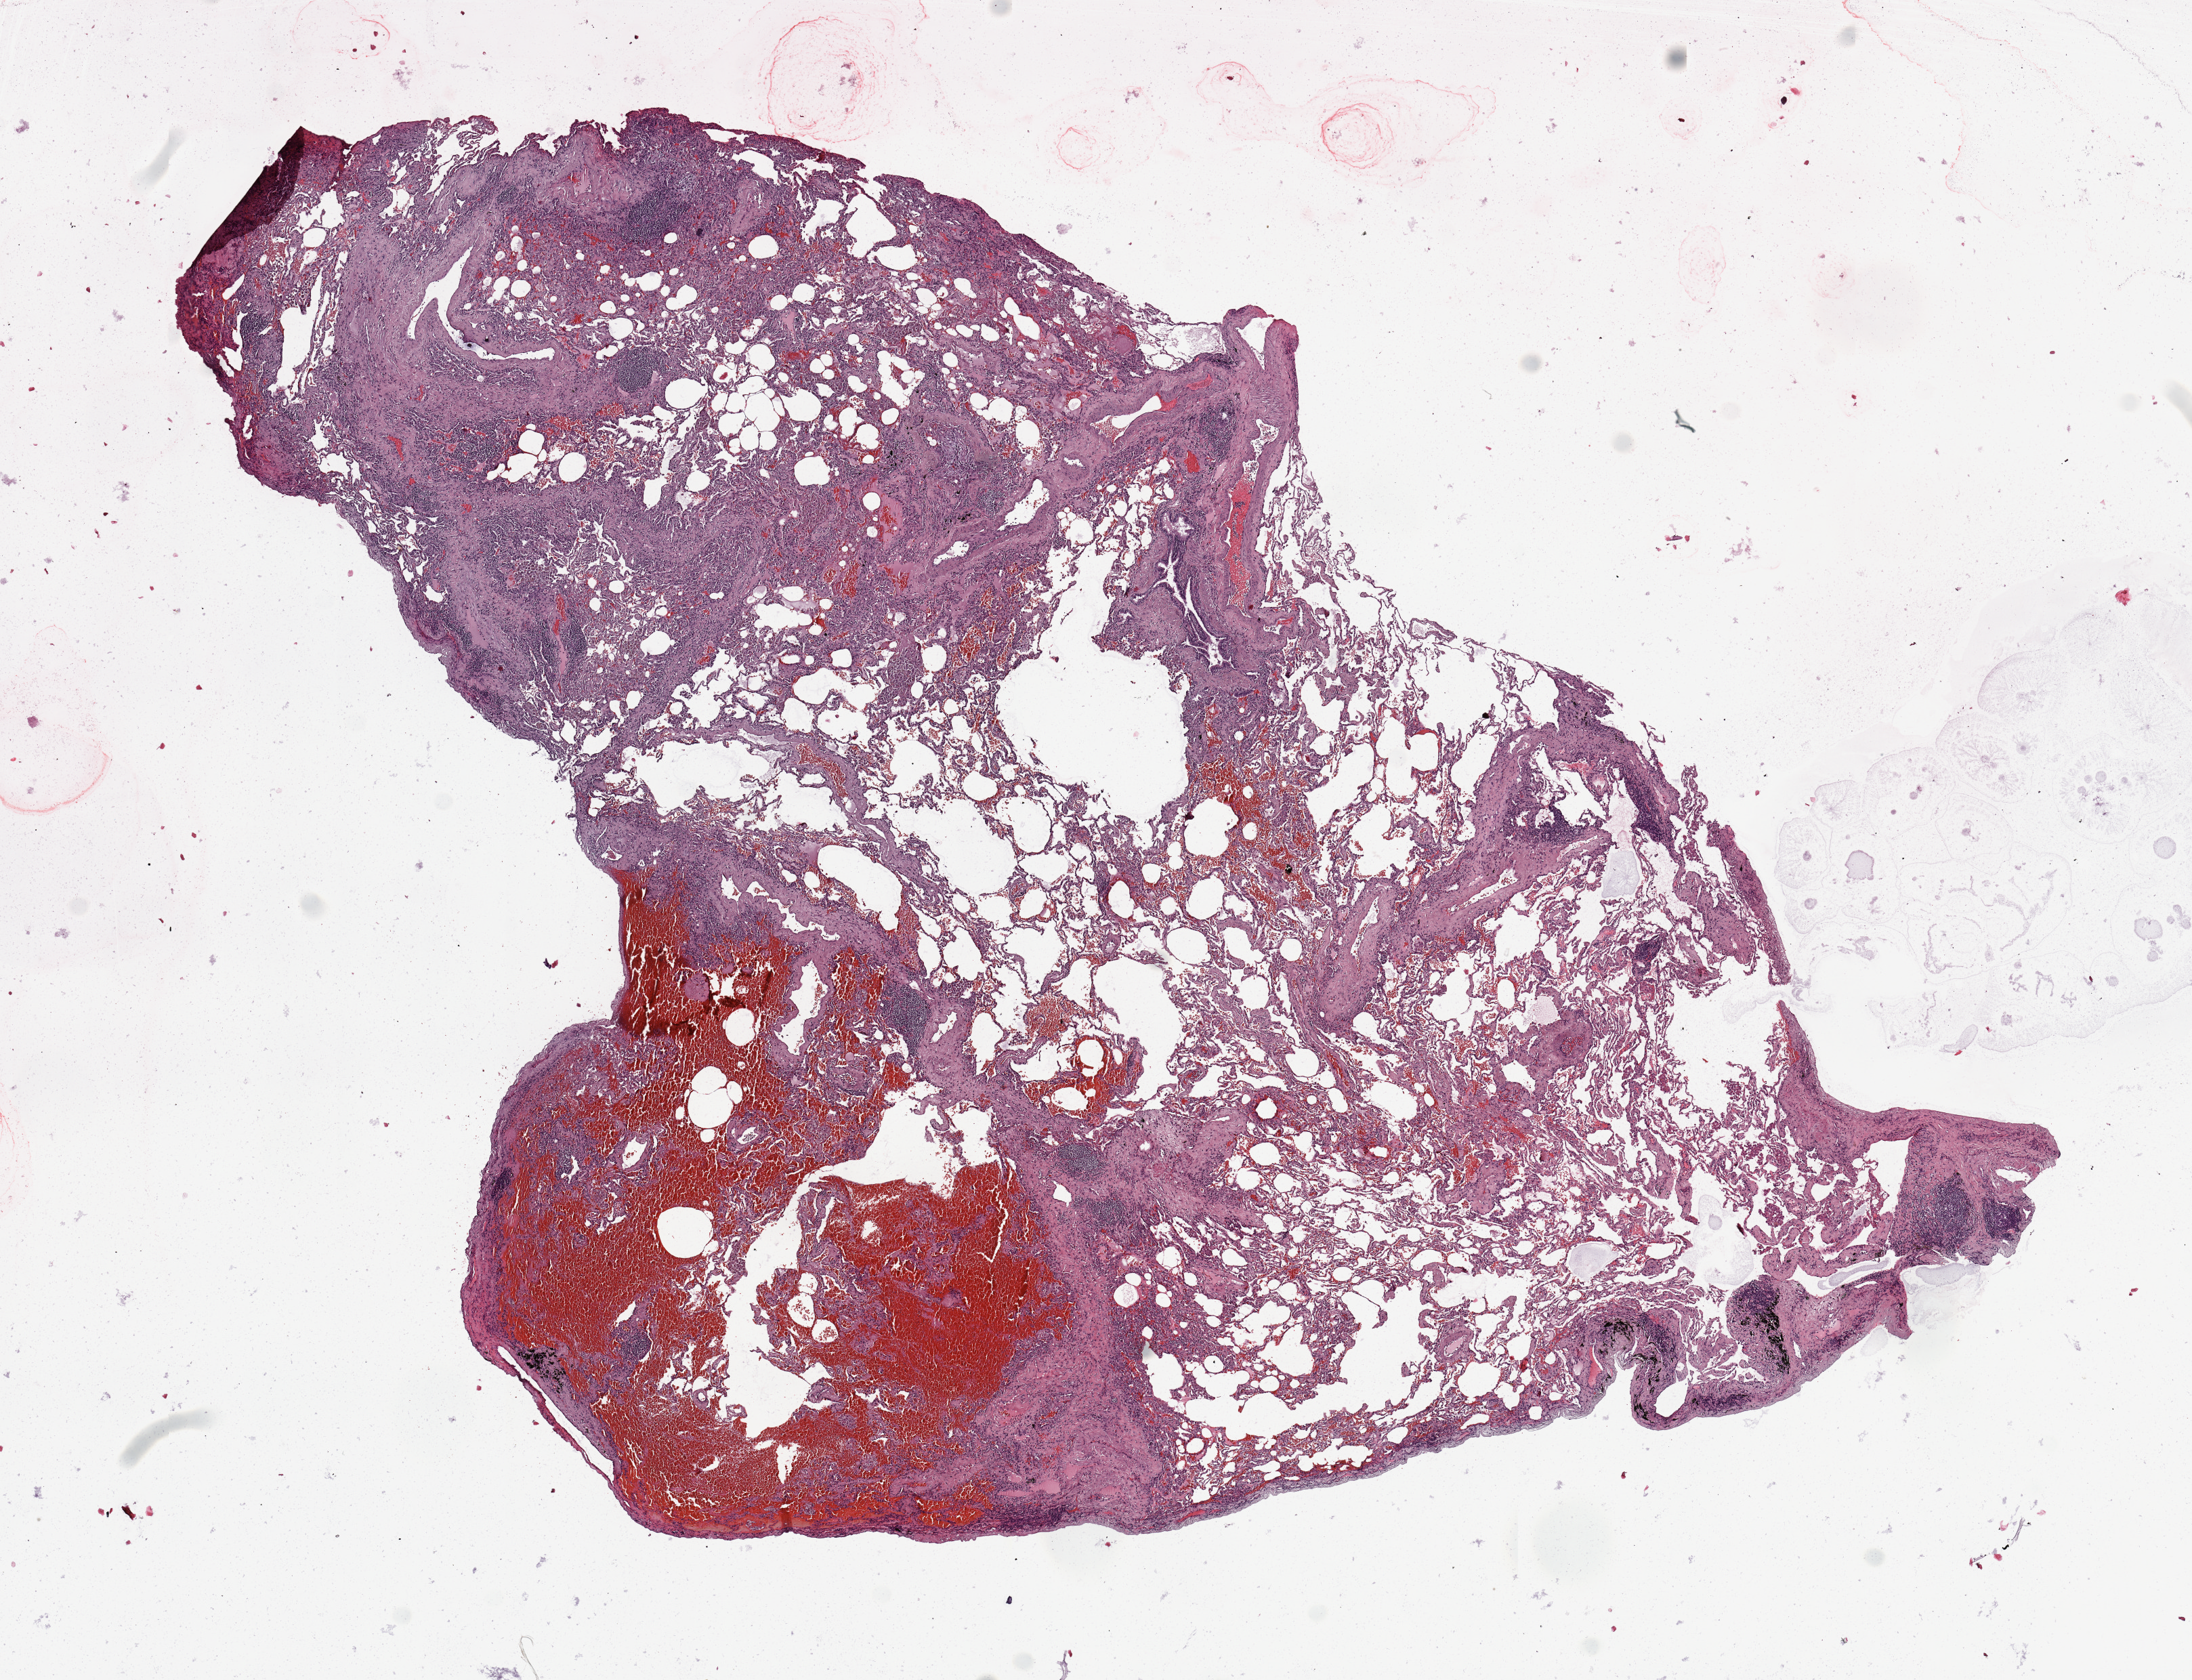
H&E whole-slide image — a low-resolution overview of the entire scanned area, about 12.8 x 9.8 mm (slide scanned at 20x), lung, normal (non-tumour) tissue. 58-year-old male patient.
- this section: normal (non-tumour) tissue from the same patient
- patient diagnosis: Squamous cell carcinoma, NOS